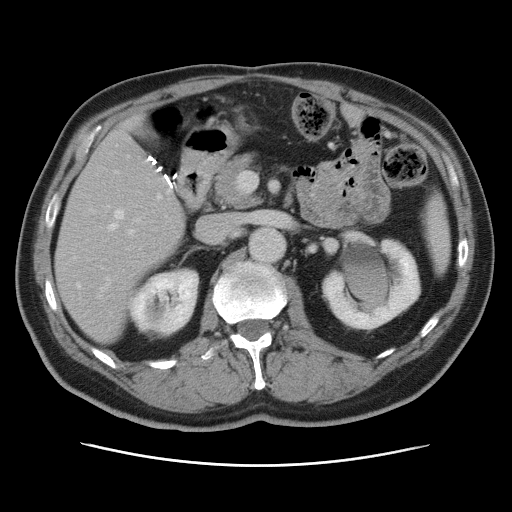
Contrast-enhanced abdominal CT, one axial slice. 120 kVp. Intravenous contrast given. Soft-tissue window (W 400 / L 40 HU). 5 mm slice thickness. 512 × 512 image matrix, field of view 370 × 370 mm. Male patient, age 69 years. Case-level facts recorded for this patient, not image findings: diagnosis: colorectal cancer liver metastases, imaged before liver resection; multiple liver metastases: no; largest metastasis: 5 cm; disease in both lobes: yes.
Annotated regions visible in this slice (expert manual segmentation):
- hepatic veins: box from (x=76, y=210) to (x=139, y=315) px
- liver: (x=56, y=116)–(x=185, y=342)
- planned liver remnant (the part of the liver to remain after resection): (x=56, y=193)–(x=186, y=342)
- portal vein (with intrahepatic branches): (x=101, y=171)–(x=134, y=292)